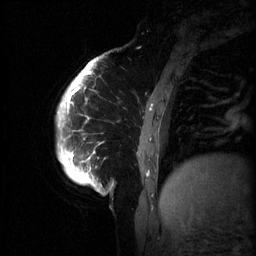
Breast MRI (dynamic contrast-enhanced), one sagittal slice. 3 images stored at this slice position (order not interpretable as contrast timing). 1.5 T. TE 4.2 ms, TR 11 ms. 2 mm slice thickness. 256 × 256 image matrix, field of view 220 × 220 mm. Patient: female, 51 years.
Annotated regions visible in this slice (semi-automatic segmentation, software-assisted and operator-edited):
- analysis volume of interest (the breast-tissue region the enhancement analysis was run in; not a lesion): bounding box <63,80,182,199> (left, top, right, bottom; pixels)
- tumour enhancement mask (voxels above the 70 % enhancement threshold inside the analysis volume of interest): <67,86,152,187>